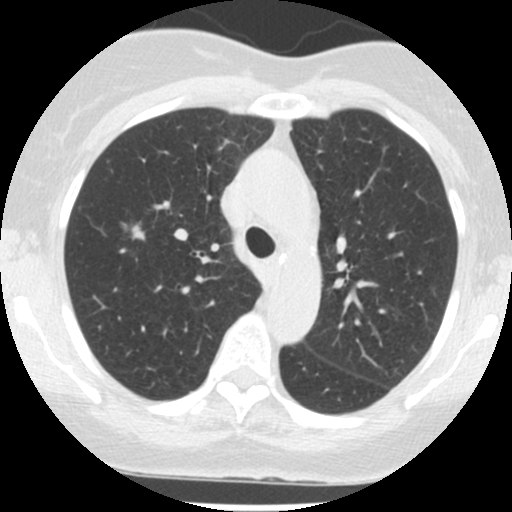
Low-dose screening chest CT, axial slice, second annual screen, lung window (W 1500 / L -600 HU), standard (soft-tissue) reconstruction kernel (STANDARD), 120 kVp, slice 29 of 99 in the series. Female participant, aged 62 years at enrolment. Former smoker at enrolment.
• Lesion marked by an expert reader, bounding box (x1, y1, x2, y2) in pixels: (108, 211, 157, 254).
• Screening reader's record for this exam (one nodule recorded; not confirmed to be the boxed lesion): non-calcified nodule or mass ≥4 mm, right upper lobe, 10 × 6 mm, spiculated (stellate) margins, soft tissue attenuation, pre-existing on the prior screen: yes; interval growth: yes.
• Lung cancer was diagnosed 515 days after this screen: adenocarcinoma, NOS, right upper lobe, well differentiated (G1), stage IA (AJCC 6th edition), 7 mm at pathology.